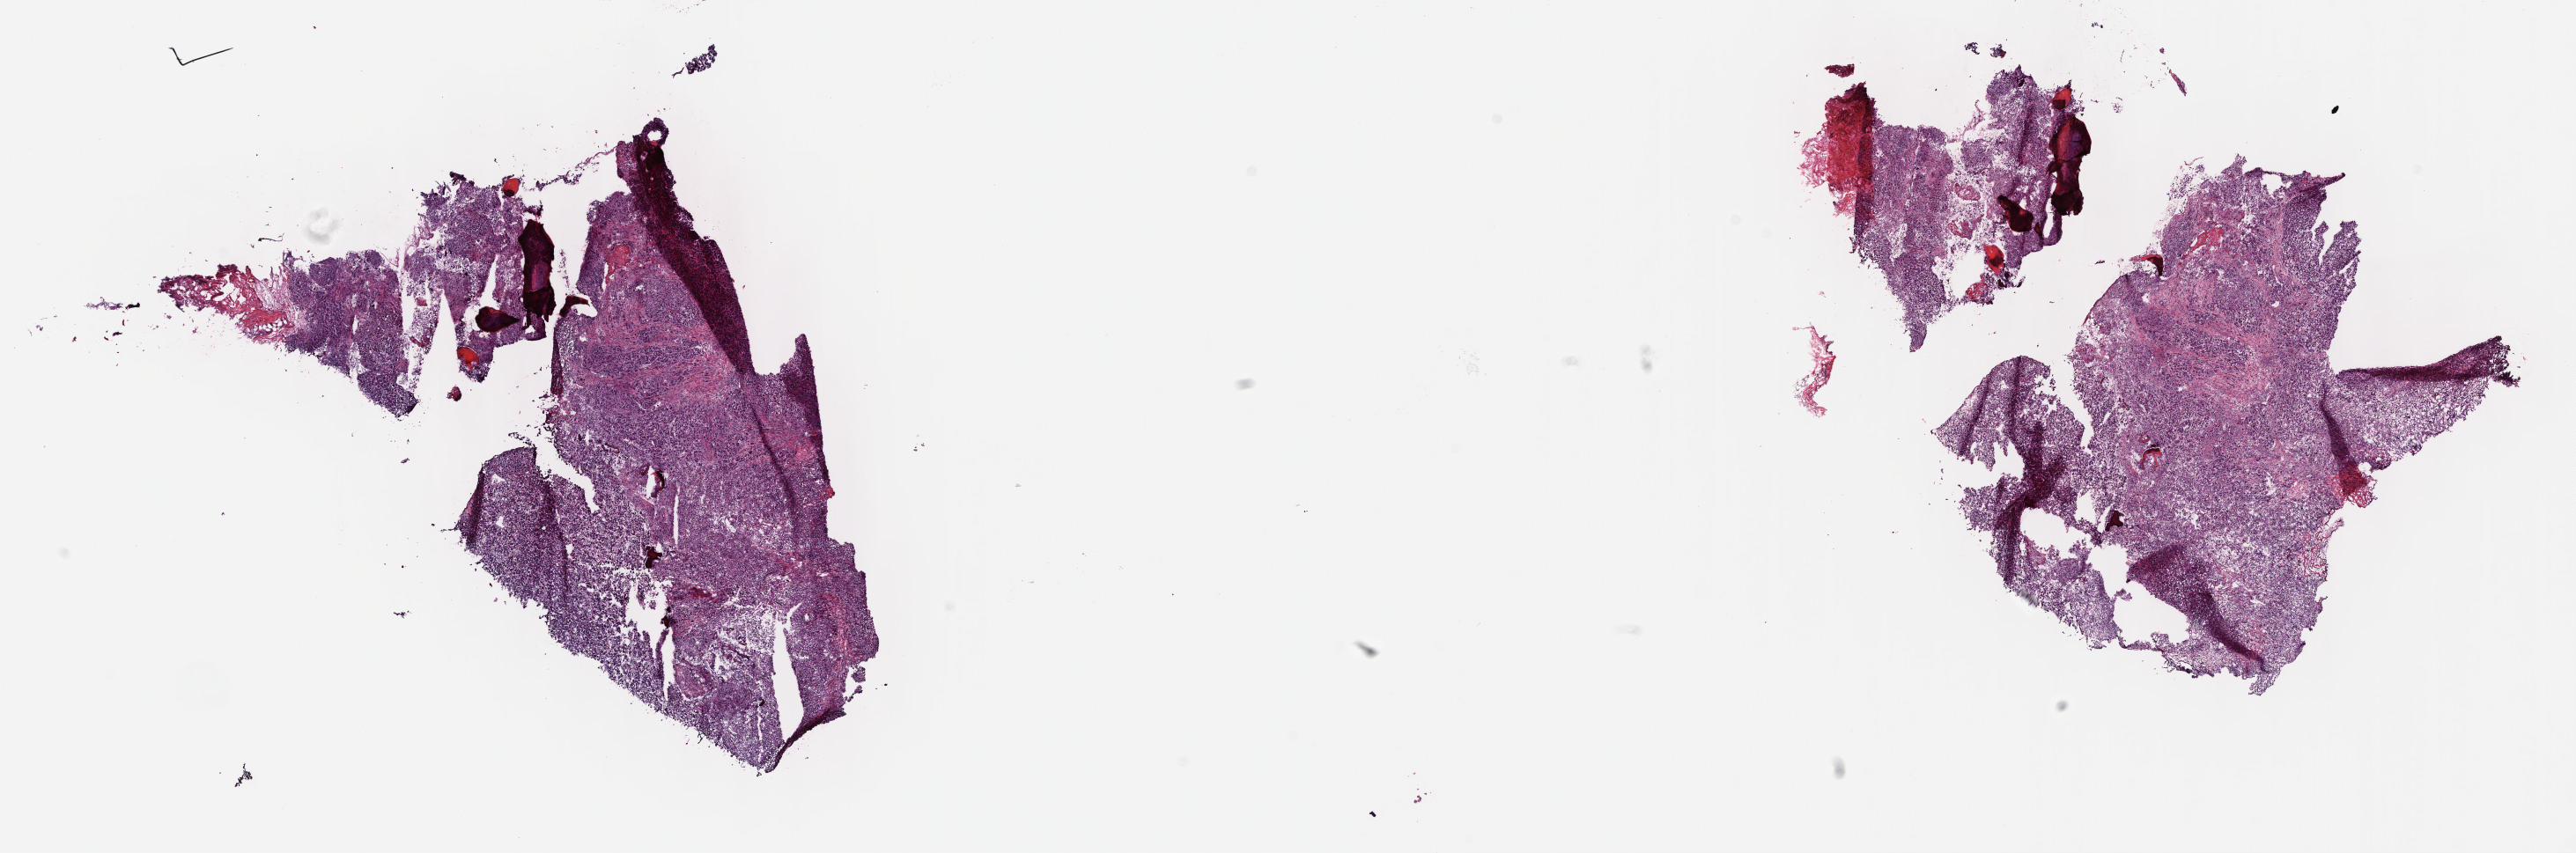
Whole-slide histology image, H&E-stained — low-resolution overview of the scanned area, about 23.7 x 7.8 mm. Frozen section from the top of the tissue portion. Metastatic tumour sample, sampled site: bones of skull and face and associated joints. Female patient. Slide review estimates, as recorded: tumour cells 80%, tumour nuclei 60%, normal cells 0%, stromal cells 0%, necrosis 20%. Inflammatory infiltration, as recorded: lymphocyte infiltration 0%, monocyte infiltration 0%, neutrophil infiltration 0%.
- this section: metastatic tumour tissue
- patient diagnosis: Malignant melanoma, NOS